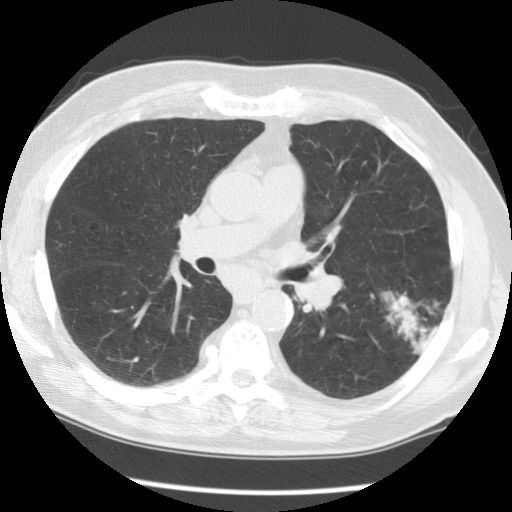
Low-dose screening chest CT, one axial slice. Position 77 of 130 along the scan axis. Reconstruction kernel STANDARD. 120 kVp. Lung window (W 1500 / L -600 HU). 2.5 mm slice thickness. 512 × 512 image matrix, field of view 340 × 340 mm.
Structures marked on this image (manually delineated by an expert):
- lesion 1 (tumor, lower lobe of left lung): box from (x=383, y=292) to (x=438, y=354) px